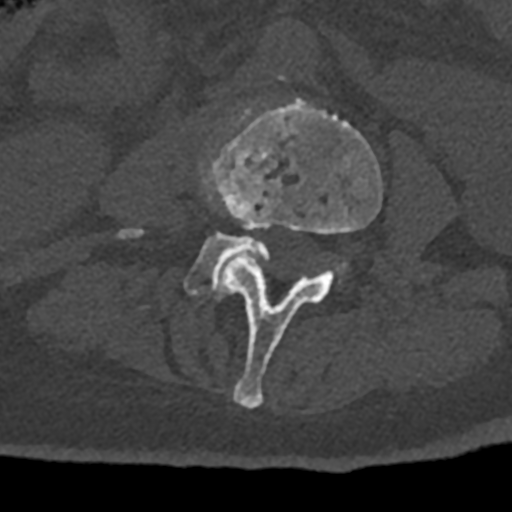
CT including the spine, one axial slice; slice 299 of 797 in the series (ordered by position); reconstruction kernel Br40s/3; 120 kVp; bone window (W 1800 / L 400 HU); 0.5 mm slice thickness; 512 × 512 image matrix, field of view 160 × 160 mm. Patient: male, 74 years. From the clinical record (not read from this slice): primary cancer: renal; vertebrae with lytic lesions (as recorded): T10, L1, L2, L3, L4, L5.
Annotated regions visible in this slice (semi-automatically segmented with operator editing):
- L3 vertebra: bounding box [x1, y1, x2, y2] px = [213, 99, 383, 408]
- L4 vertebra: [119, 229, 347, 299]